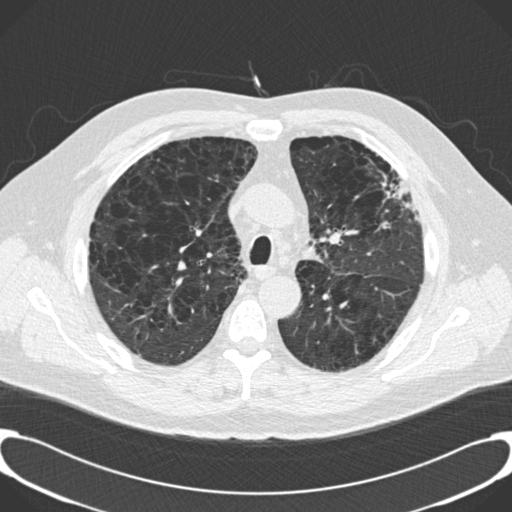
Low-dose screening chest CT, one axial slice; 120 kVp; lung window (W 1500 / L -600 HU); 2 mm slice thickness; 512 × 512 image matrix, field of view 380 × 380 mm.
Annotated regions visible in this slice (manually delineated by an expert):
- lesion 1 (tumor, upper lobe of left lung): bounding box <390,178,409,204> (left, top, right, bottom; pixels)